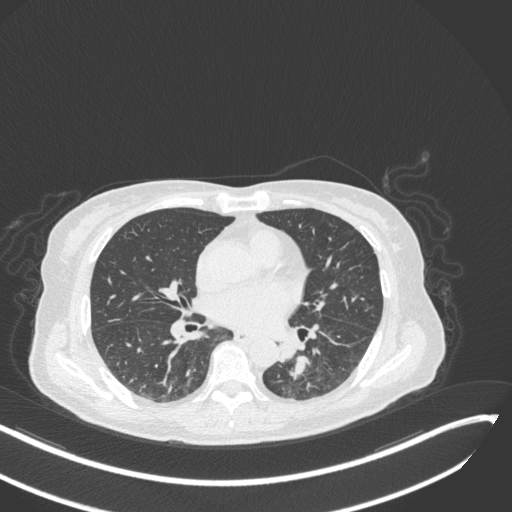
Chest CT, one axial slice; slice 128 of 342 in the series (ordered by position); reconstruction kernel B31f; lung window (W 1500 / L -600 HU); 1 mm slice thickness; 512 × 512 image matrix, field of view 400 × 400 mm. Patient: female, 64 years. Case-level facts recorded for this patient, not image findings: clinical TNM (as recorded): T3 N1 M1; histopathological grade: G3.
Outlined on this slice (rectangle marked by the reading radiologist):
- lung tumour (recorded histology: small cell carcinoma): bounding box (x1, y1, x2, y2) in pixels: (276, 339, 314, 375)